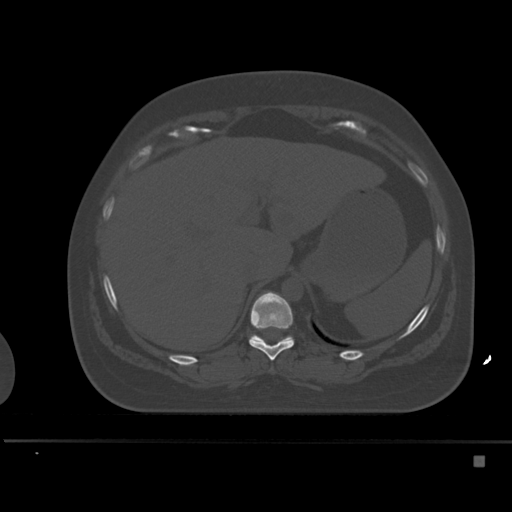
CT including the spine, one axial slice; slice 244 of 495 in the series (ordered by position); bone window (W 1800 / L 400 HU); 1.5 mm slice thickness; 512 × 512 image matrix, field of view 404 × 404 mm. Female patient, age 33 years. From the clinical record (not read from this slice): primary cancer: breast; vertebrae with lytic lesions (as recorded): T1.
Outlined on this slice (semi-automatic segmentation, software-assisted and operator-edited):
- T10 vertebra: bounding box [x1, y1, x2, y2] px = [249, 292, 294, 360]
- T11 vertebra: [250, 335, 292, 342]